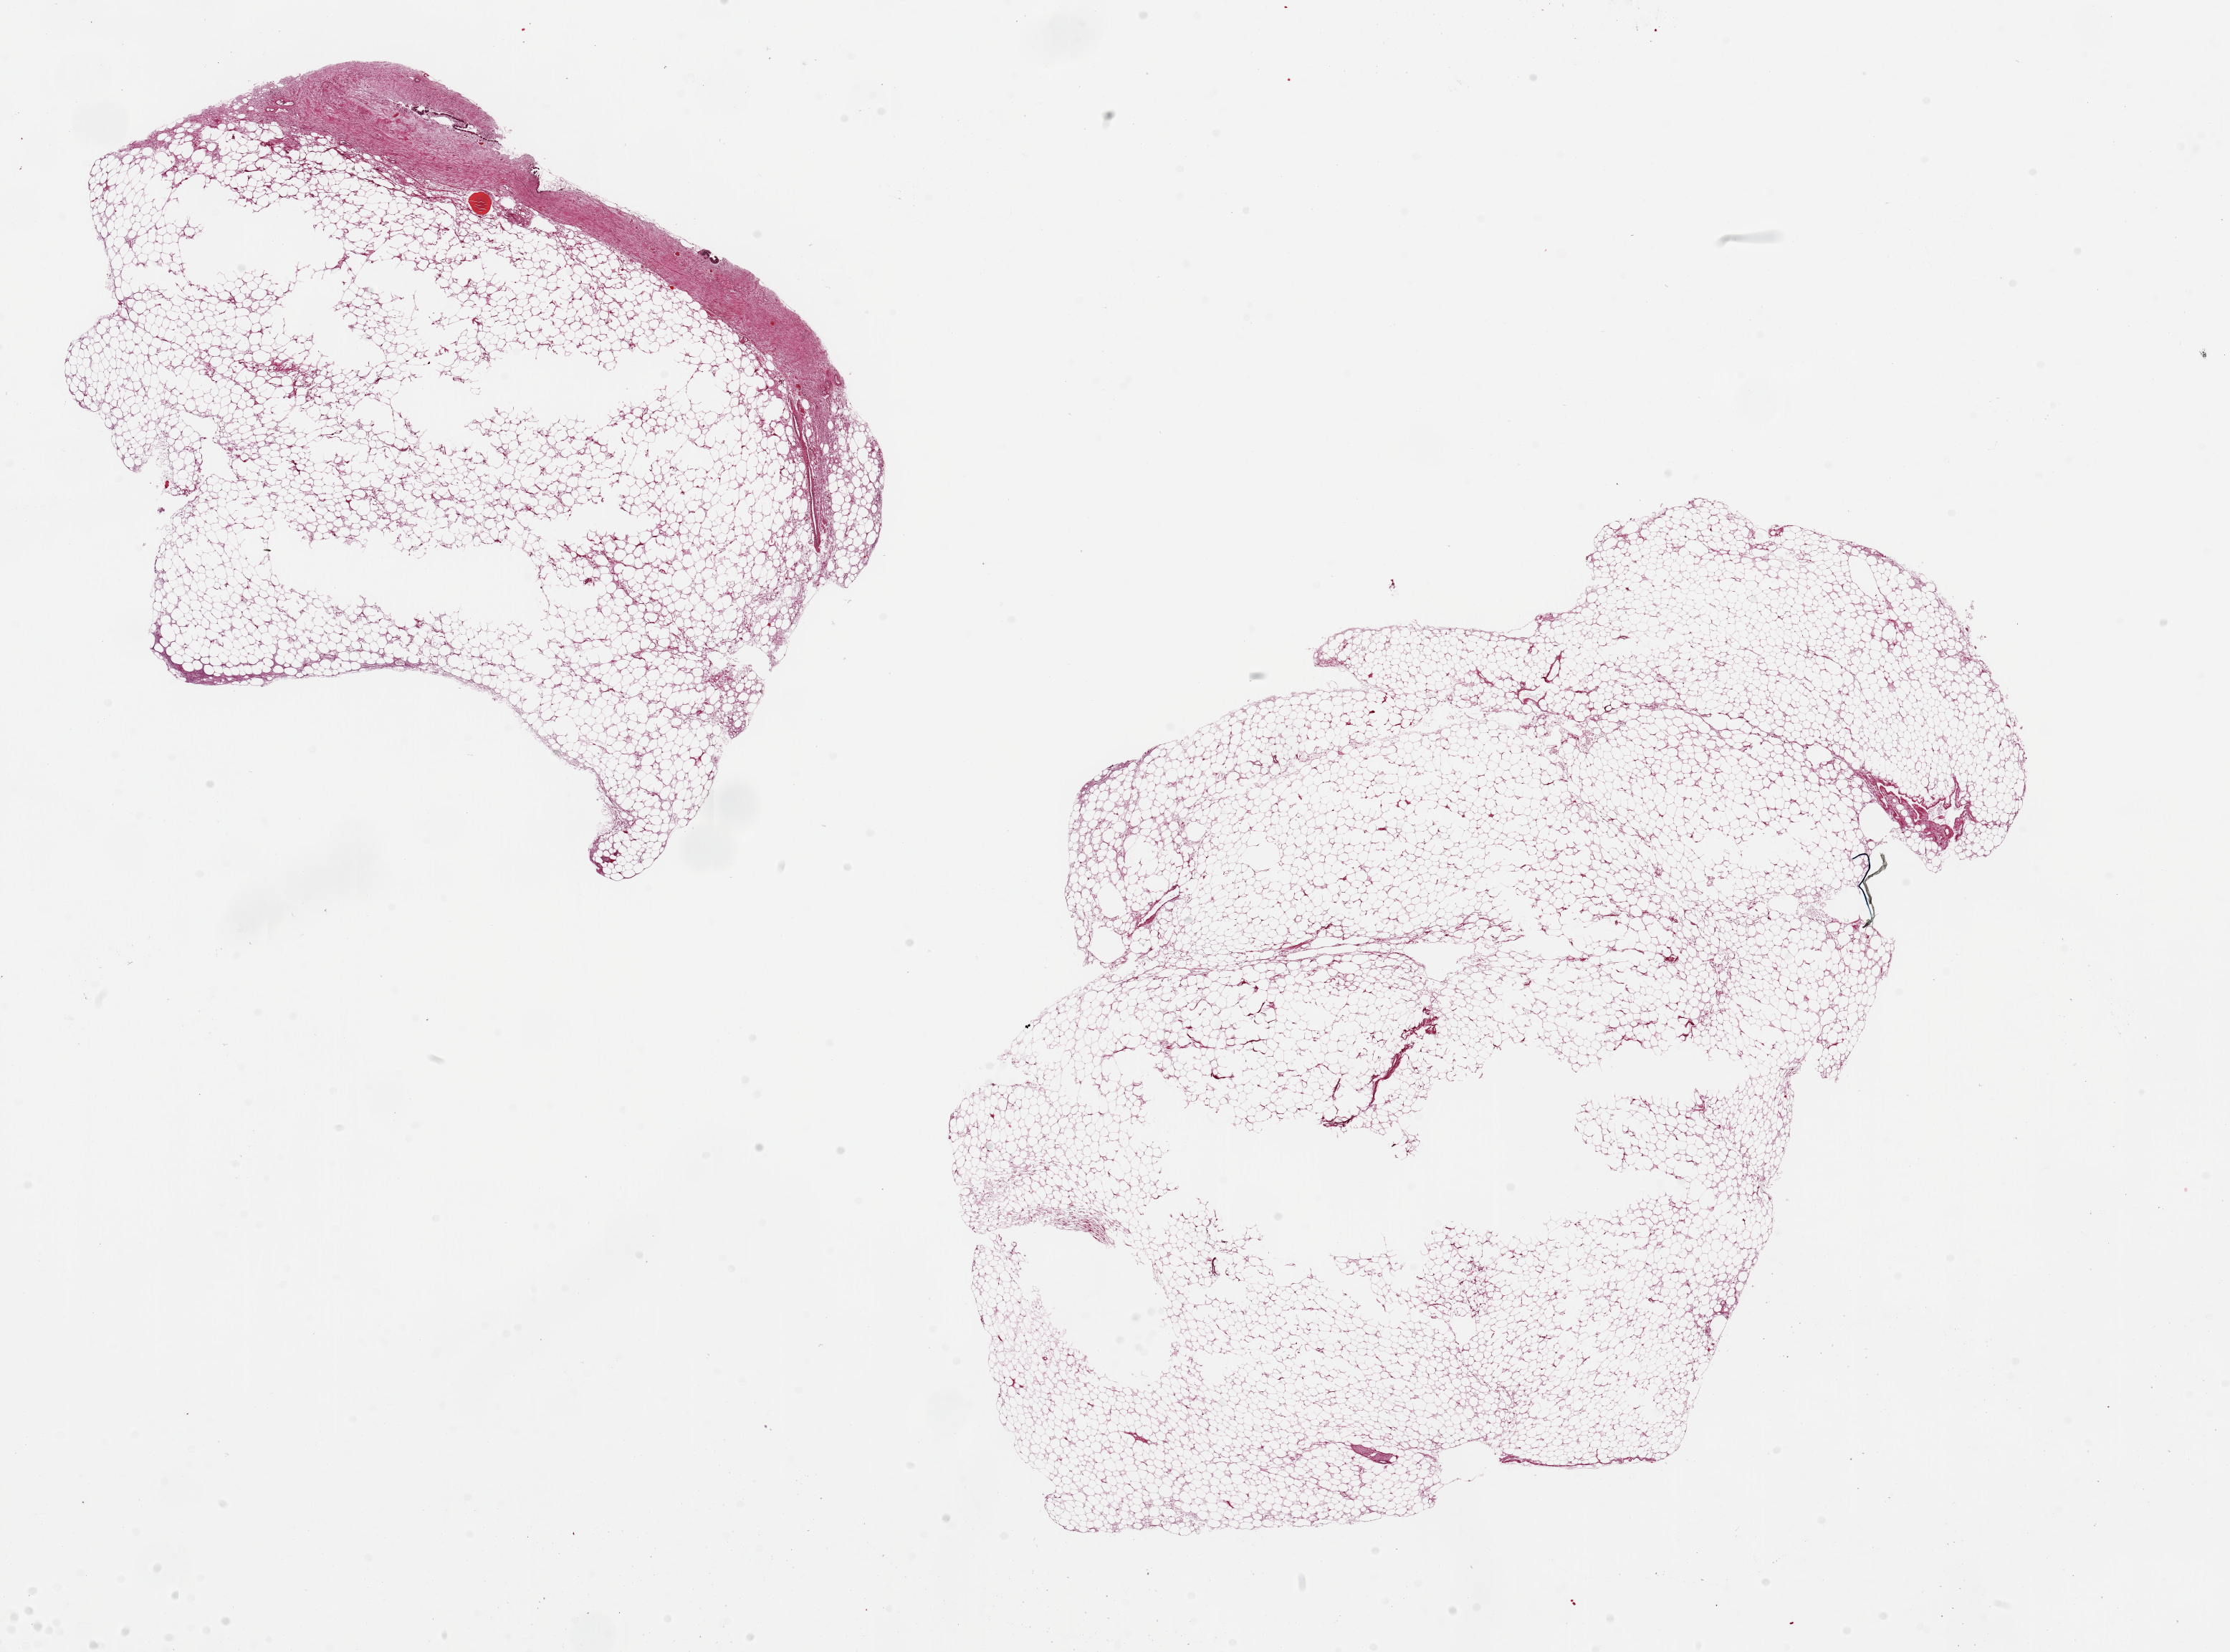
Haematoxylin and eosin whole-slide image, brightfield, shown as a low-resolution overview of the whole scanned area (about 24.6 x 18.2 mm, from a 20x scan). PAXgene-fixed, paraffin-embedded tissue. Target tissue: renal medulla. Tissue donor sample.
* review note (as recorded): 2 pieces 14x9 & 9x7 mm; virtually all adipose tissue